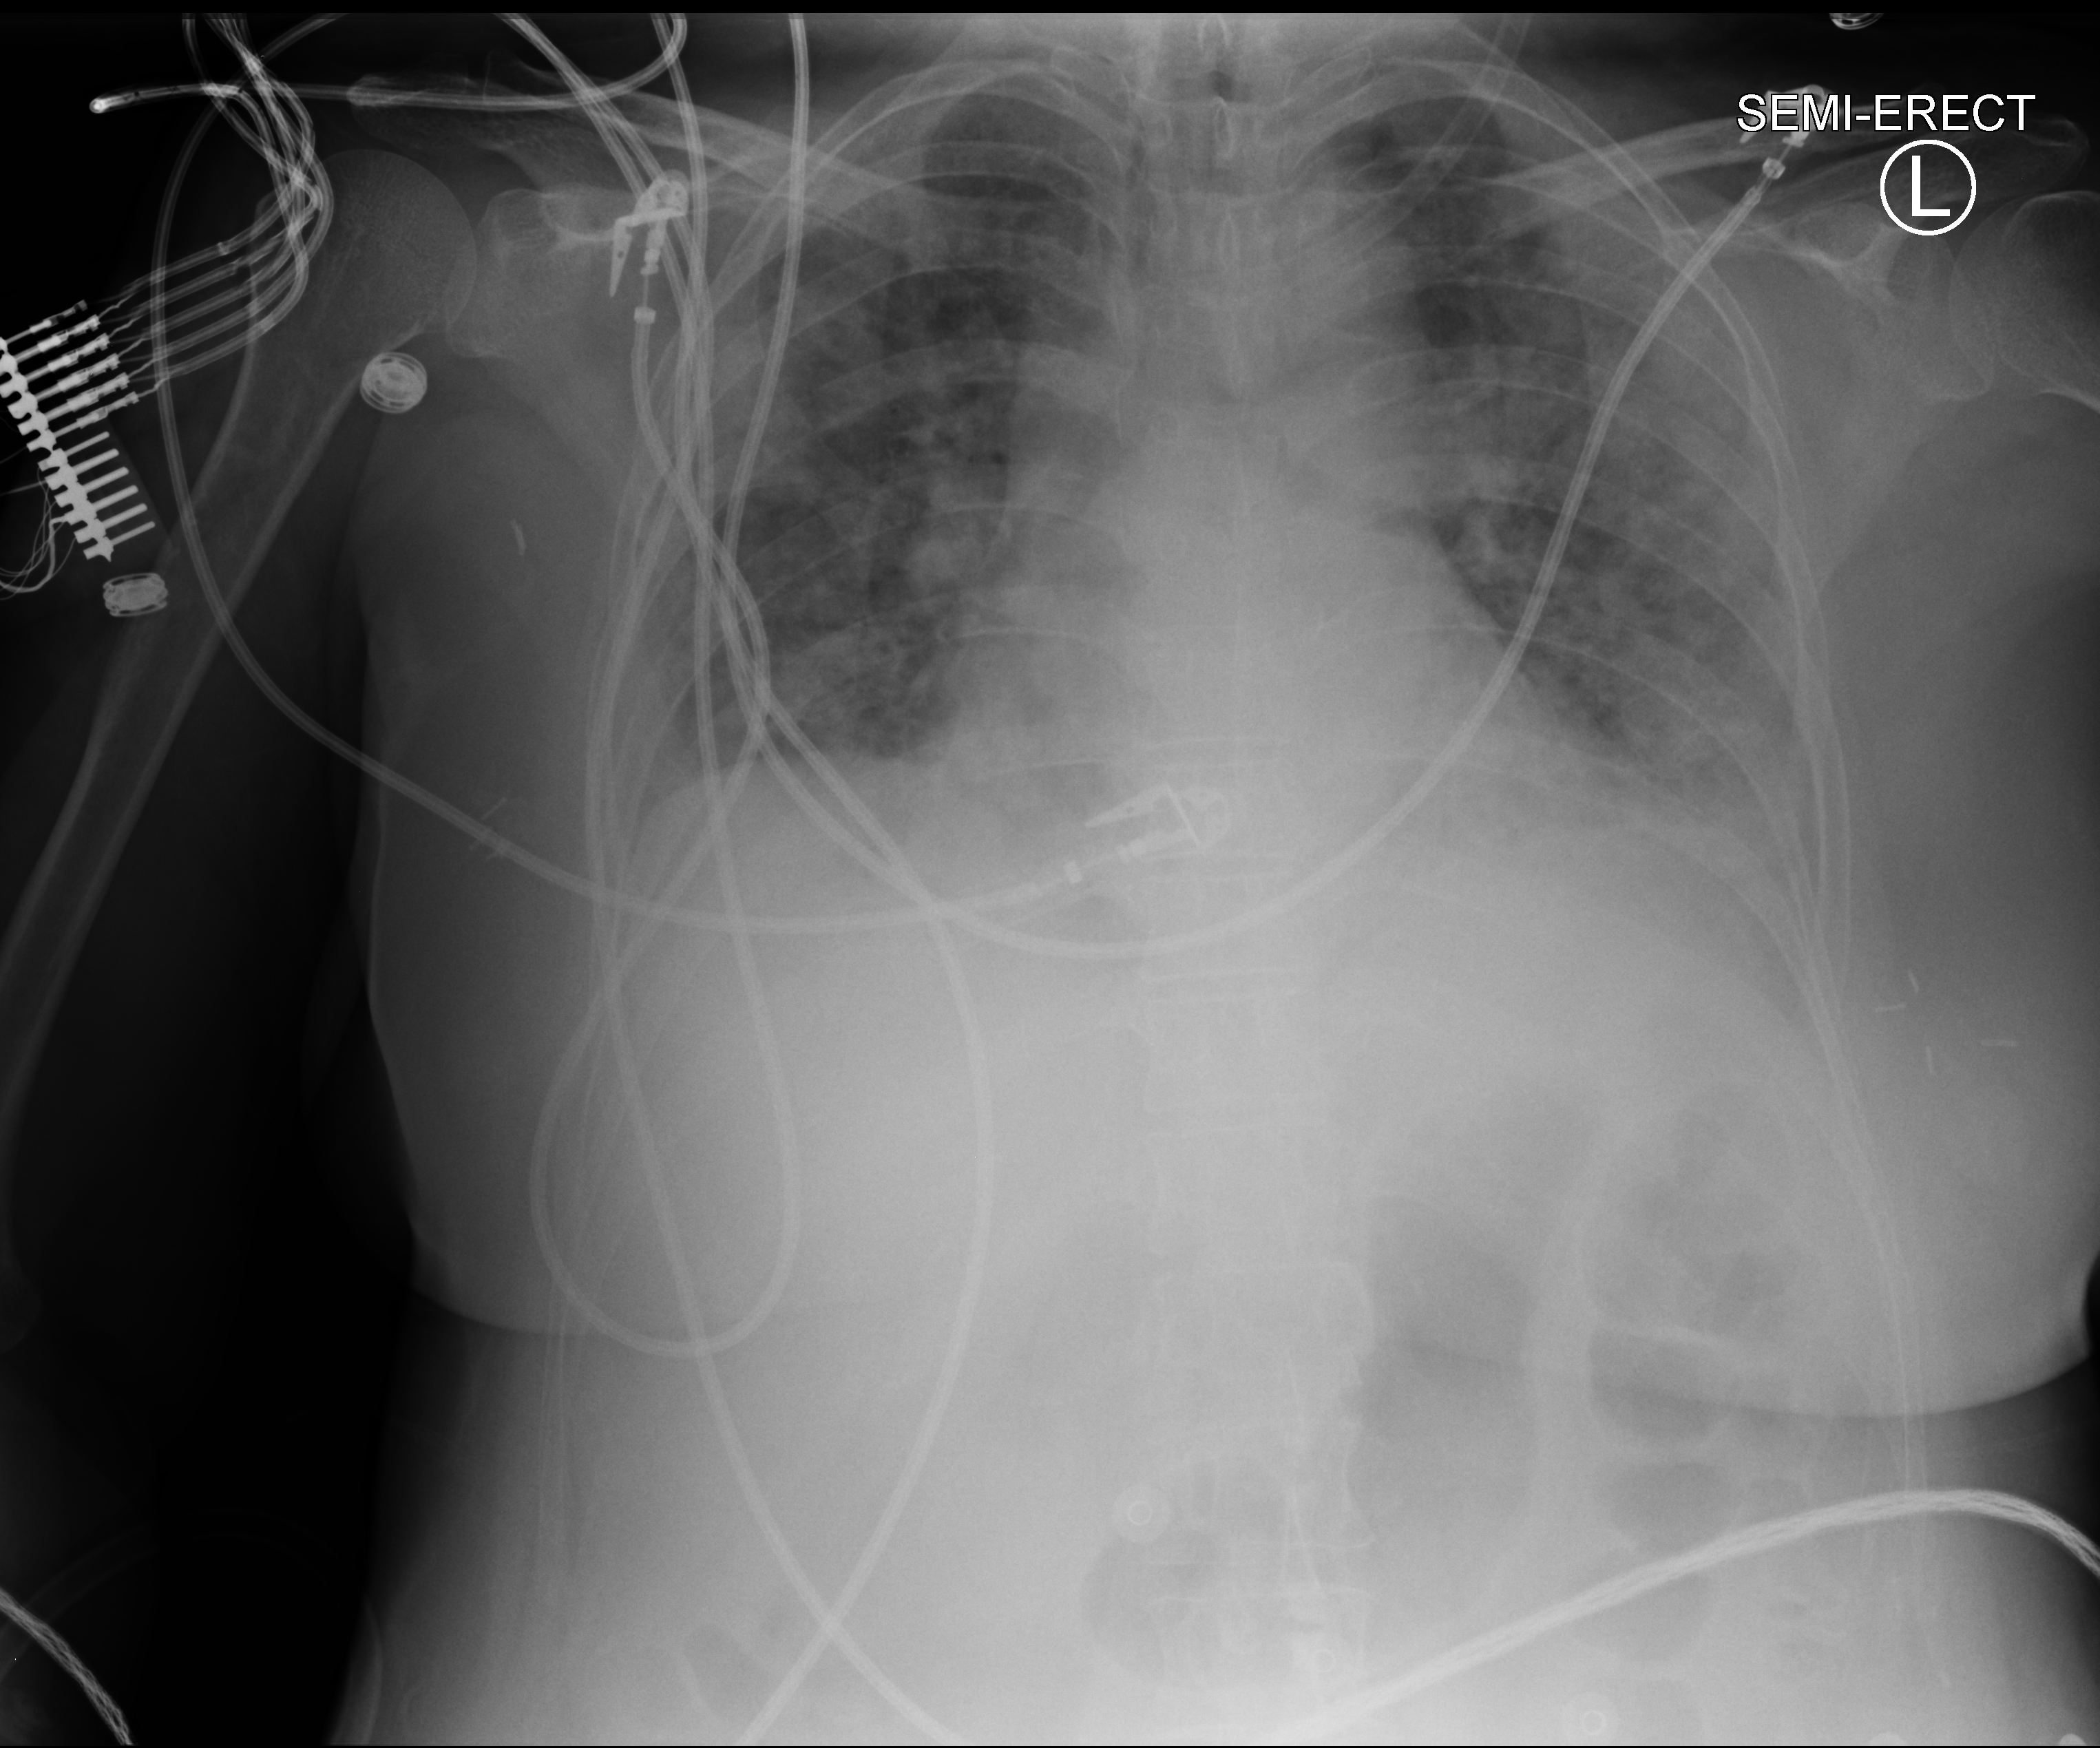
Portable chest radiograph, anteroposterior (AP) projection. Patient hospitalised with COVID-19; female, aged 18–59 years.
From the hospital-stay record, not from the radiograph (when in the stay this image was taken is not recorded): mechanically ventilated during this hospital stay: yes; admitted to intensive care during this hospital stay: no.